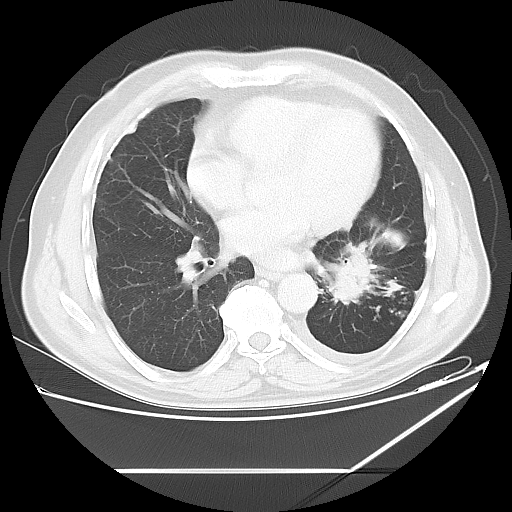
Chest CT, one axial slice; lung window (W 1500 / L -600 HU); 512 × 512 image matrix. Patient: male, 62 years. Case-level facts recorded for this patient, not image findings: clinical TNM (as recorded): T3 N0 M1.
Structures marked on this image (rectangle marked by the reading radiologist):
- lung tumour (recorded histology: adenocarcinoma): bounding box (x1, y1, x2, y2) in pixels: (325, 233, 383, 312)
- lung tumour (recorded histology: adenocarcinoma): (327, 237, 382, 311)